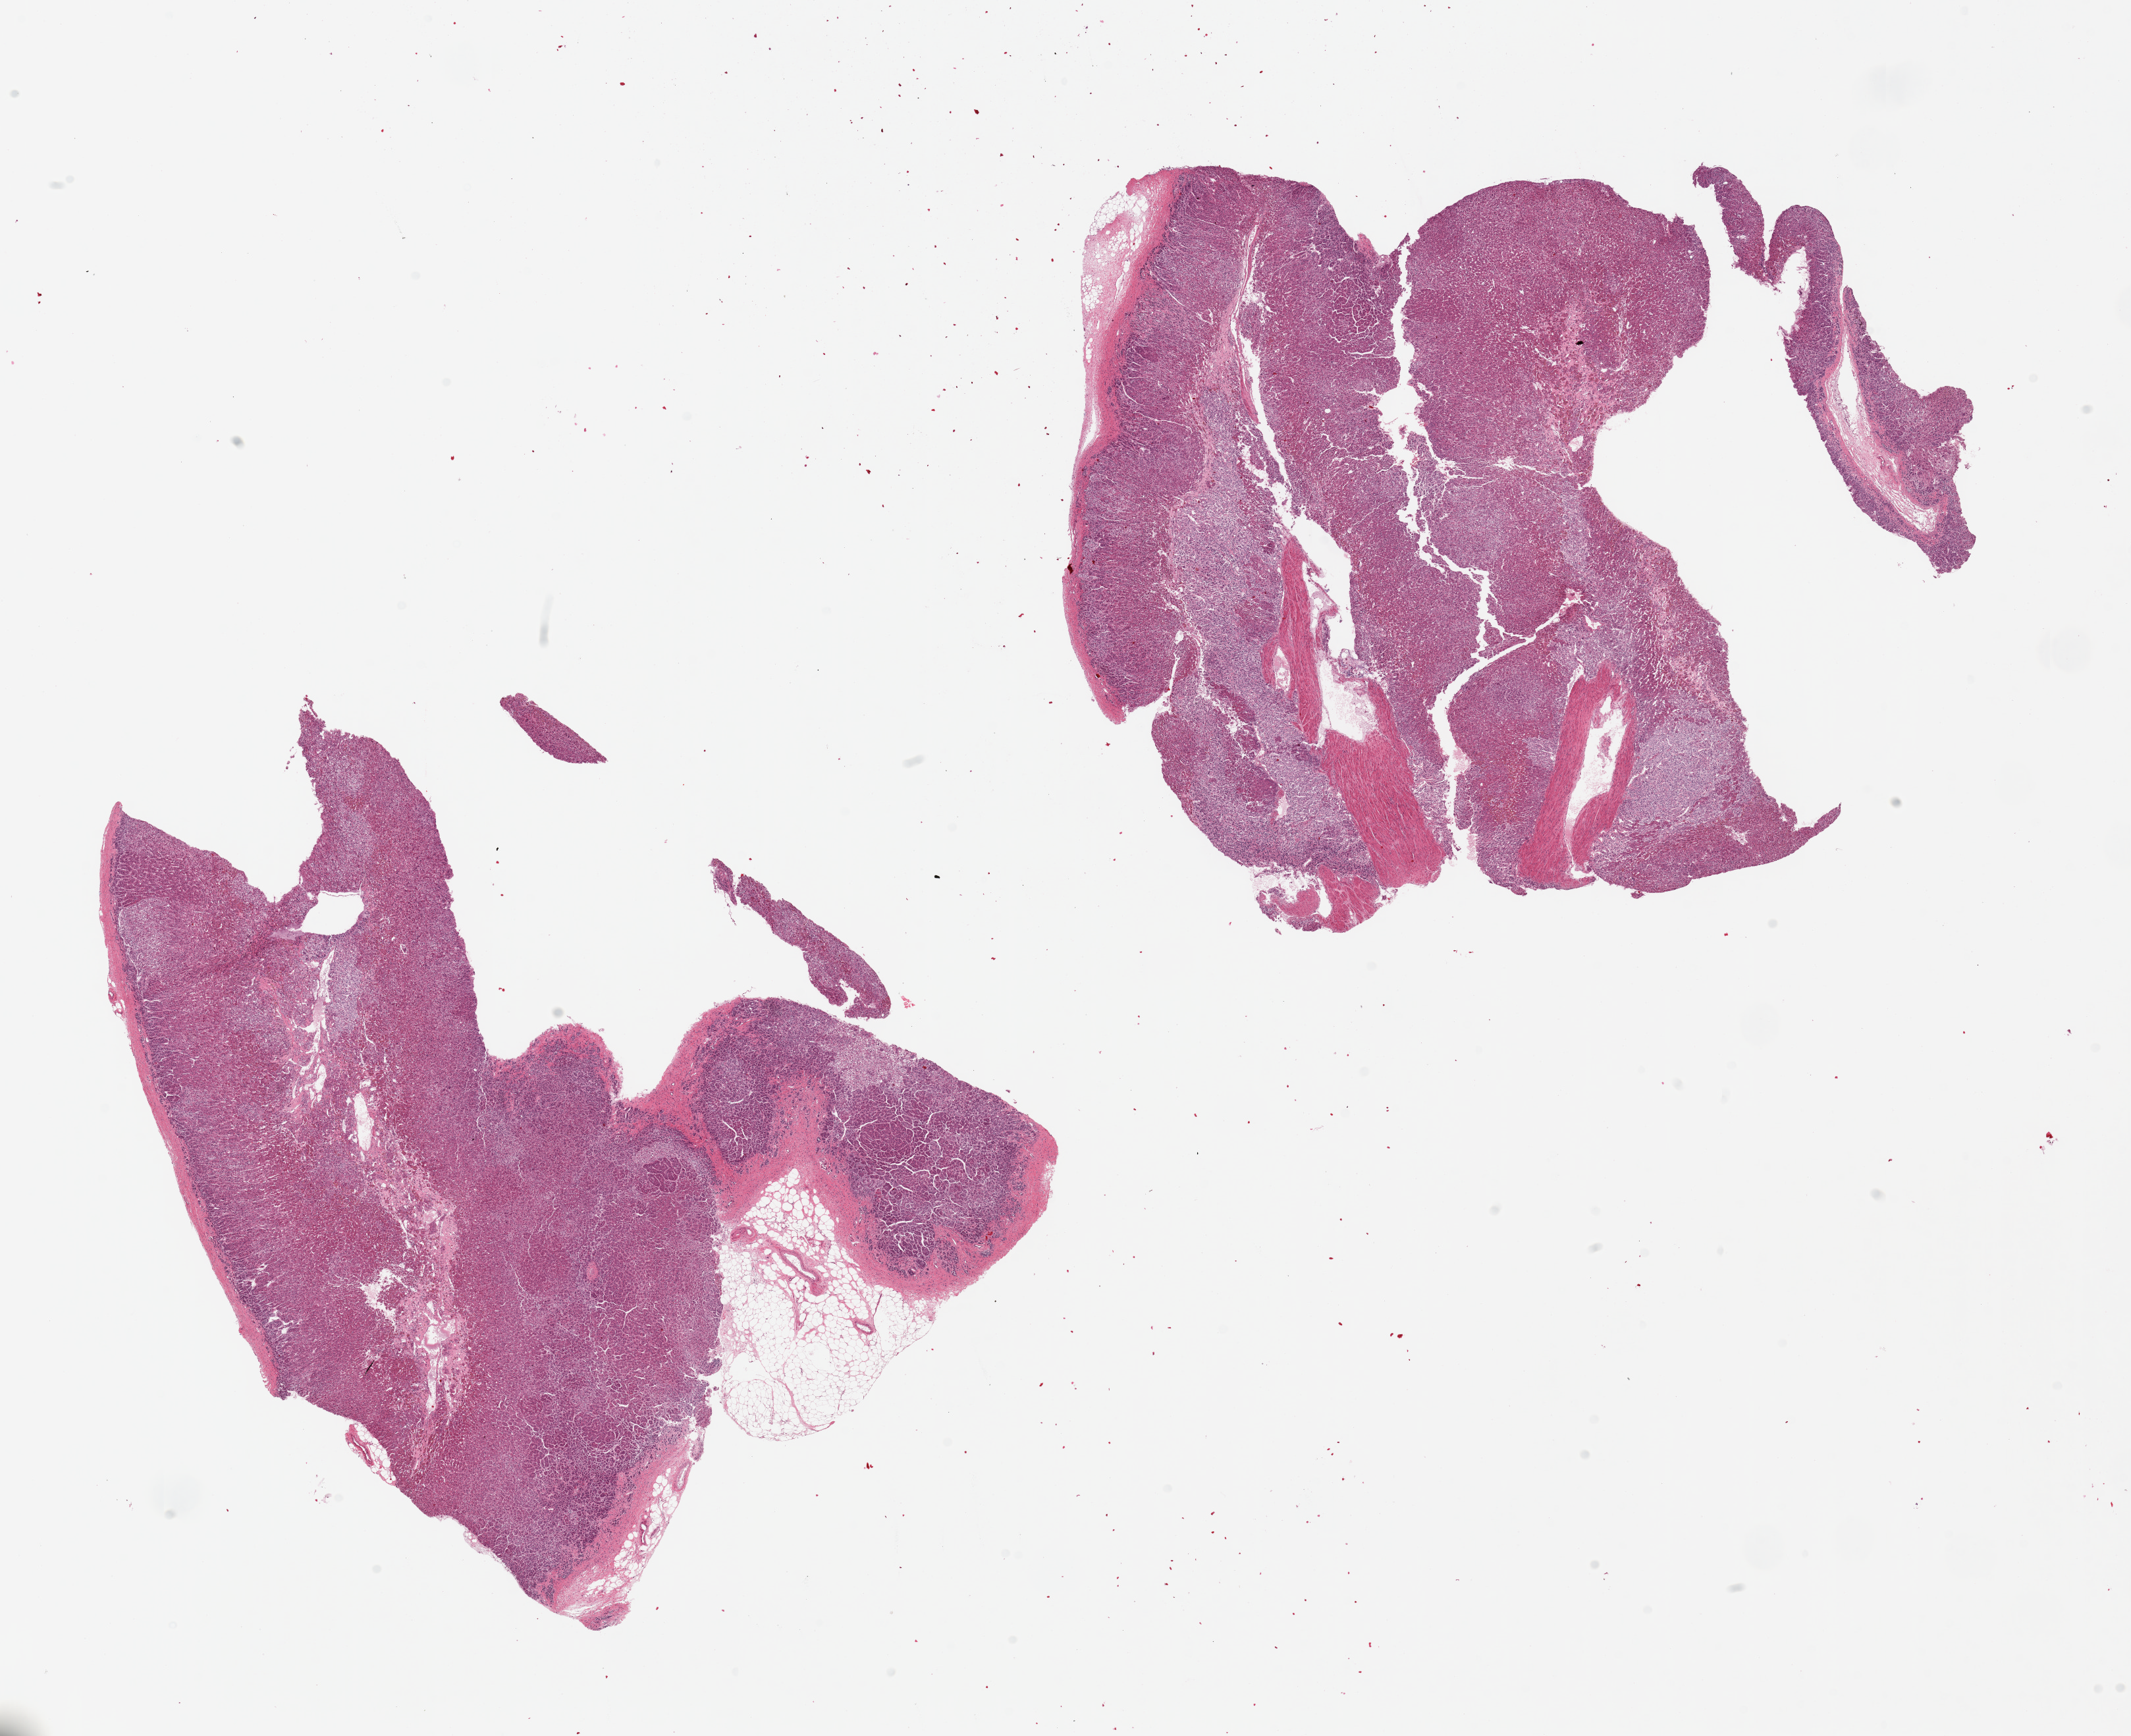
Whole-slide image, H&E stain, shown as a low-resolution overview of the whole scanned area (about 25.6 x 20.8 mm), PAXgene-fixed, paraffin-embedded tissue, sampled site (target tissue): adrenal gland, tissue donor sample. Donor: male.
Pathologist's review note for this sample: 2 pieces.